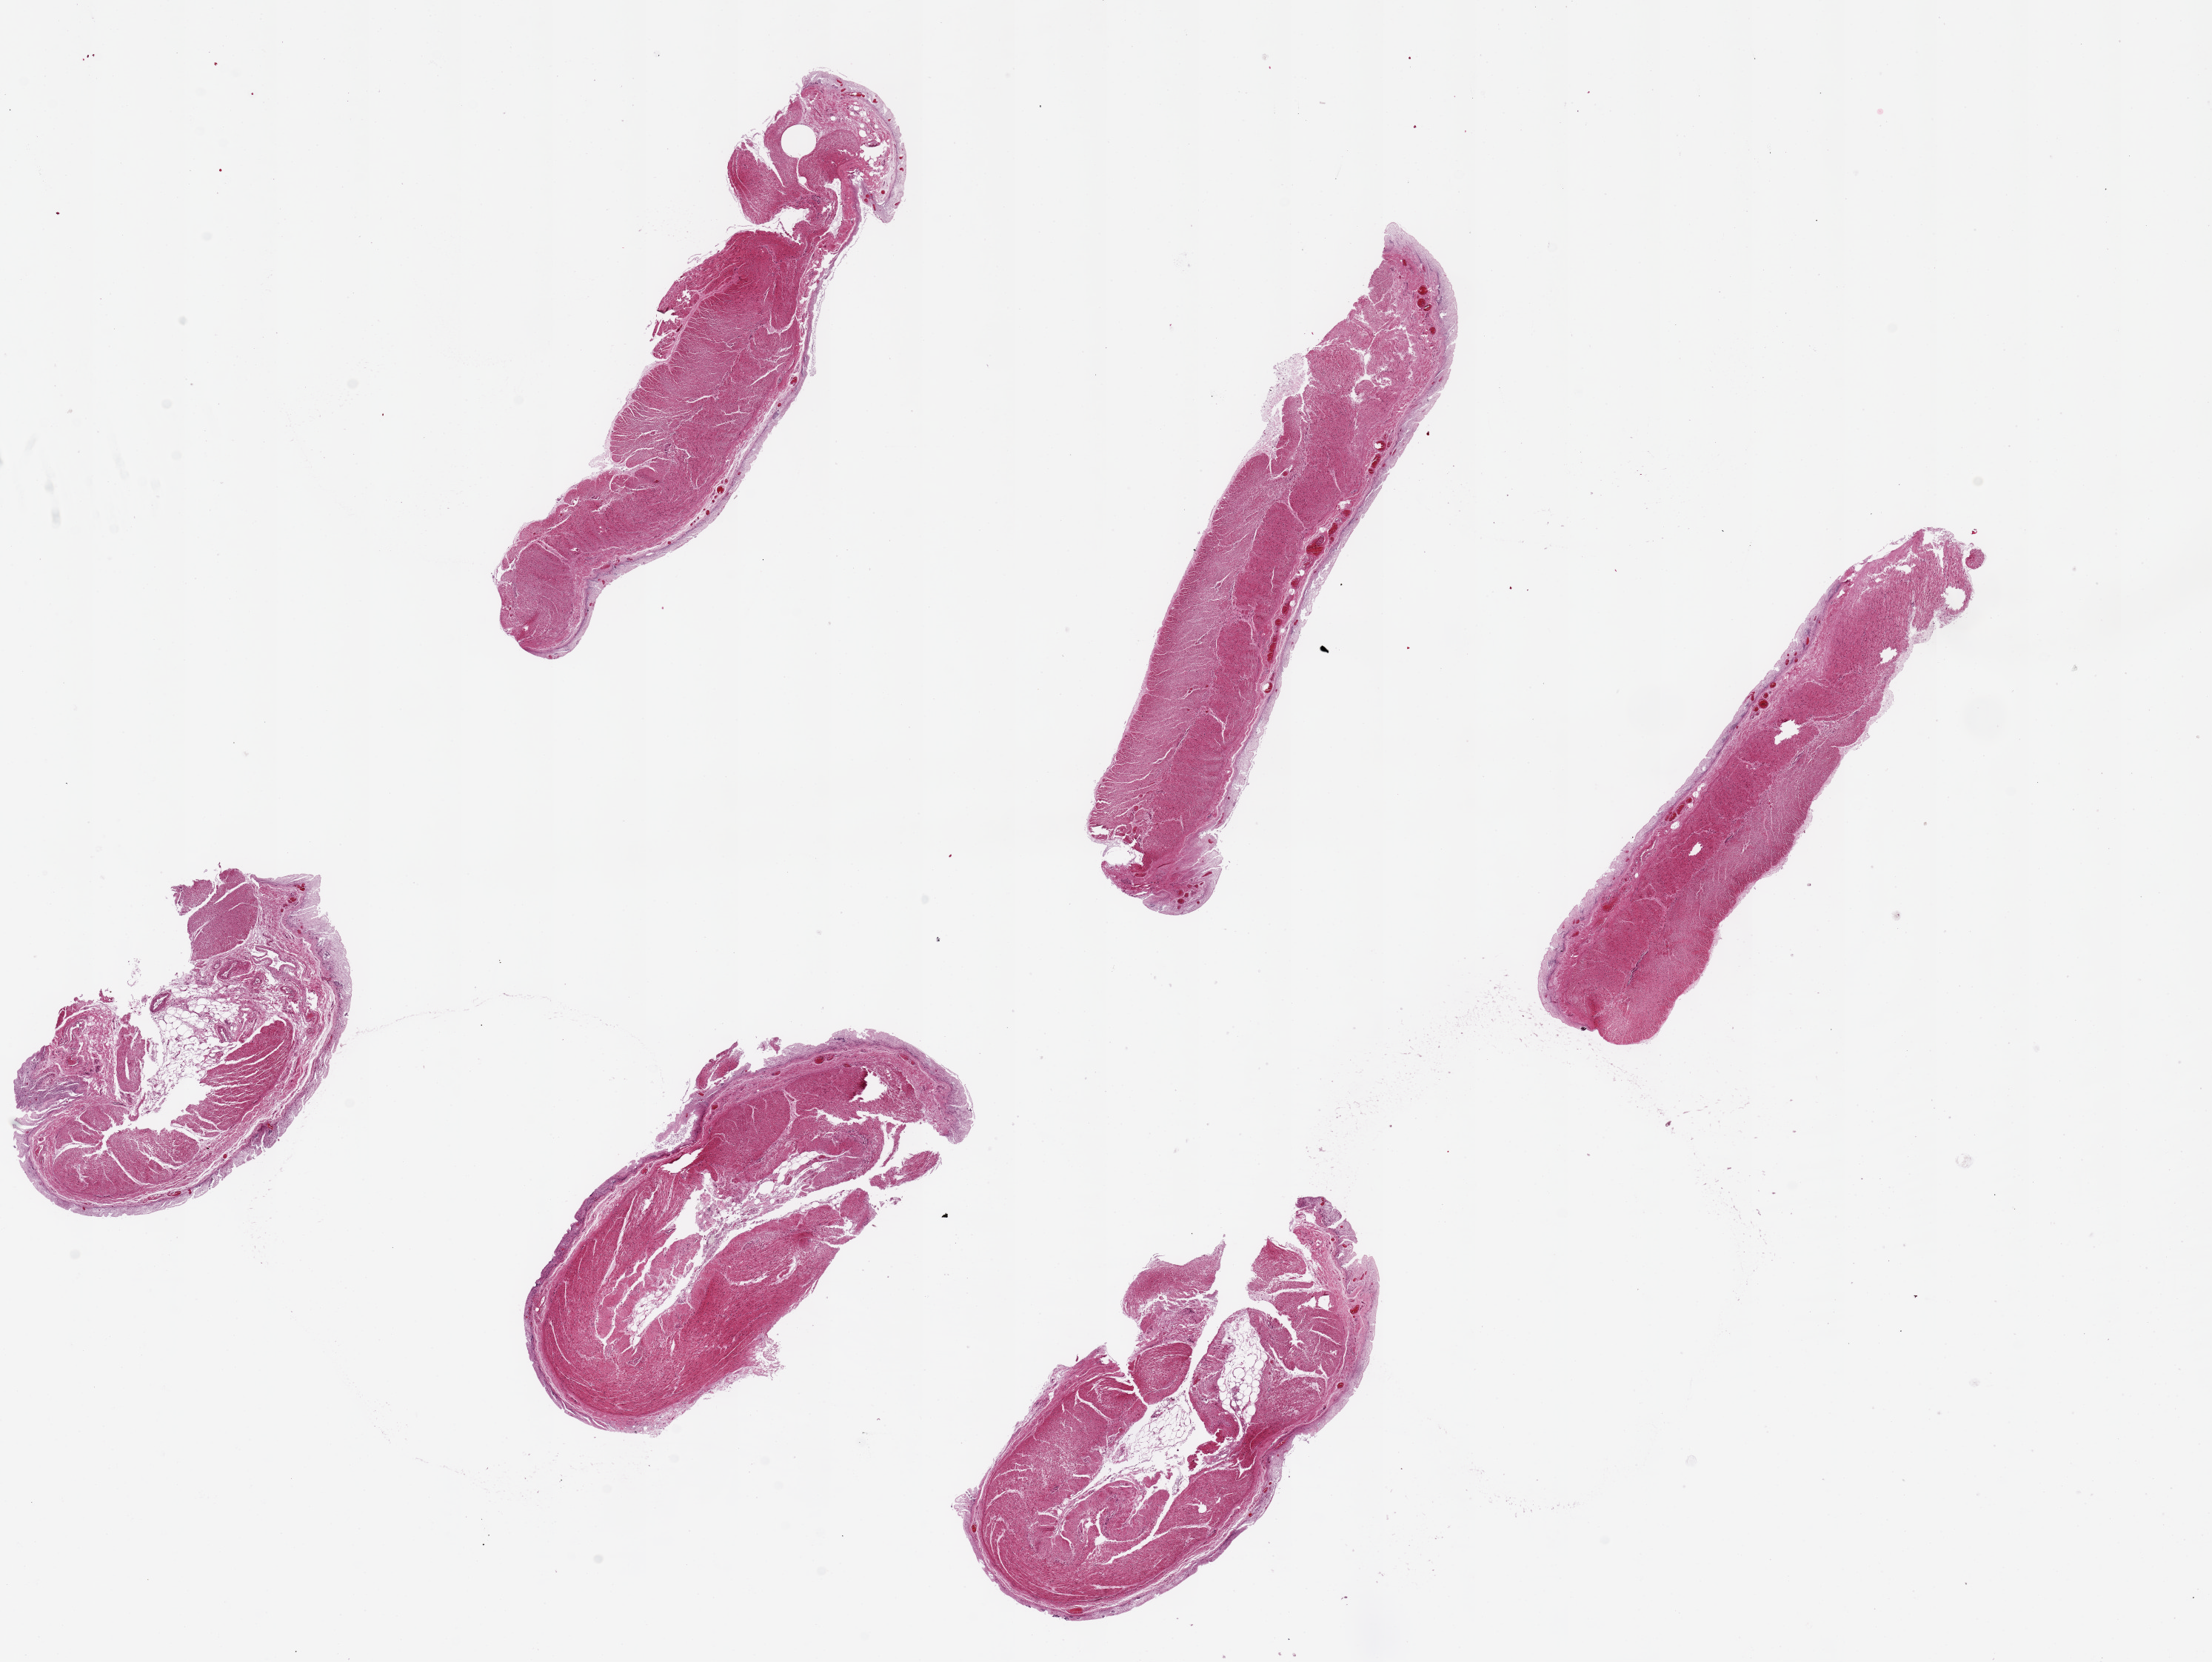
Digitized haematoxylin and eosin-stained section, a low-resolution overview of the entire scanned area, about 23.6 x 17.7 mm (slide scanned at 20x). PAXgene-fixed paraffin-embedded (PFPE) section. Target tissue: sigmoid colon. Donor tissue sample.
Pathologist's review note for this sample: 6 pieces, up to 8x1.5mm; mainly muscle less than 10% autlyzed mucosa.